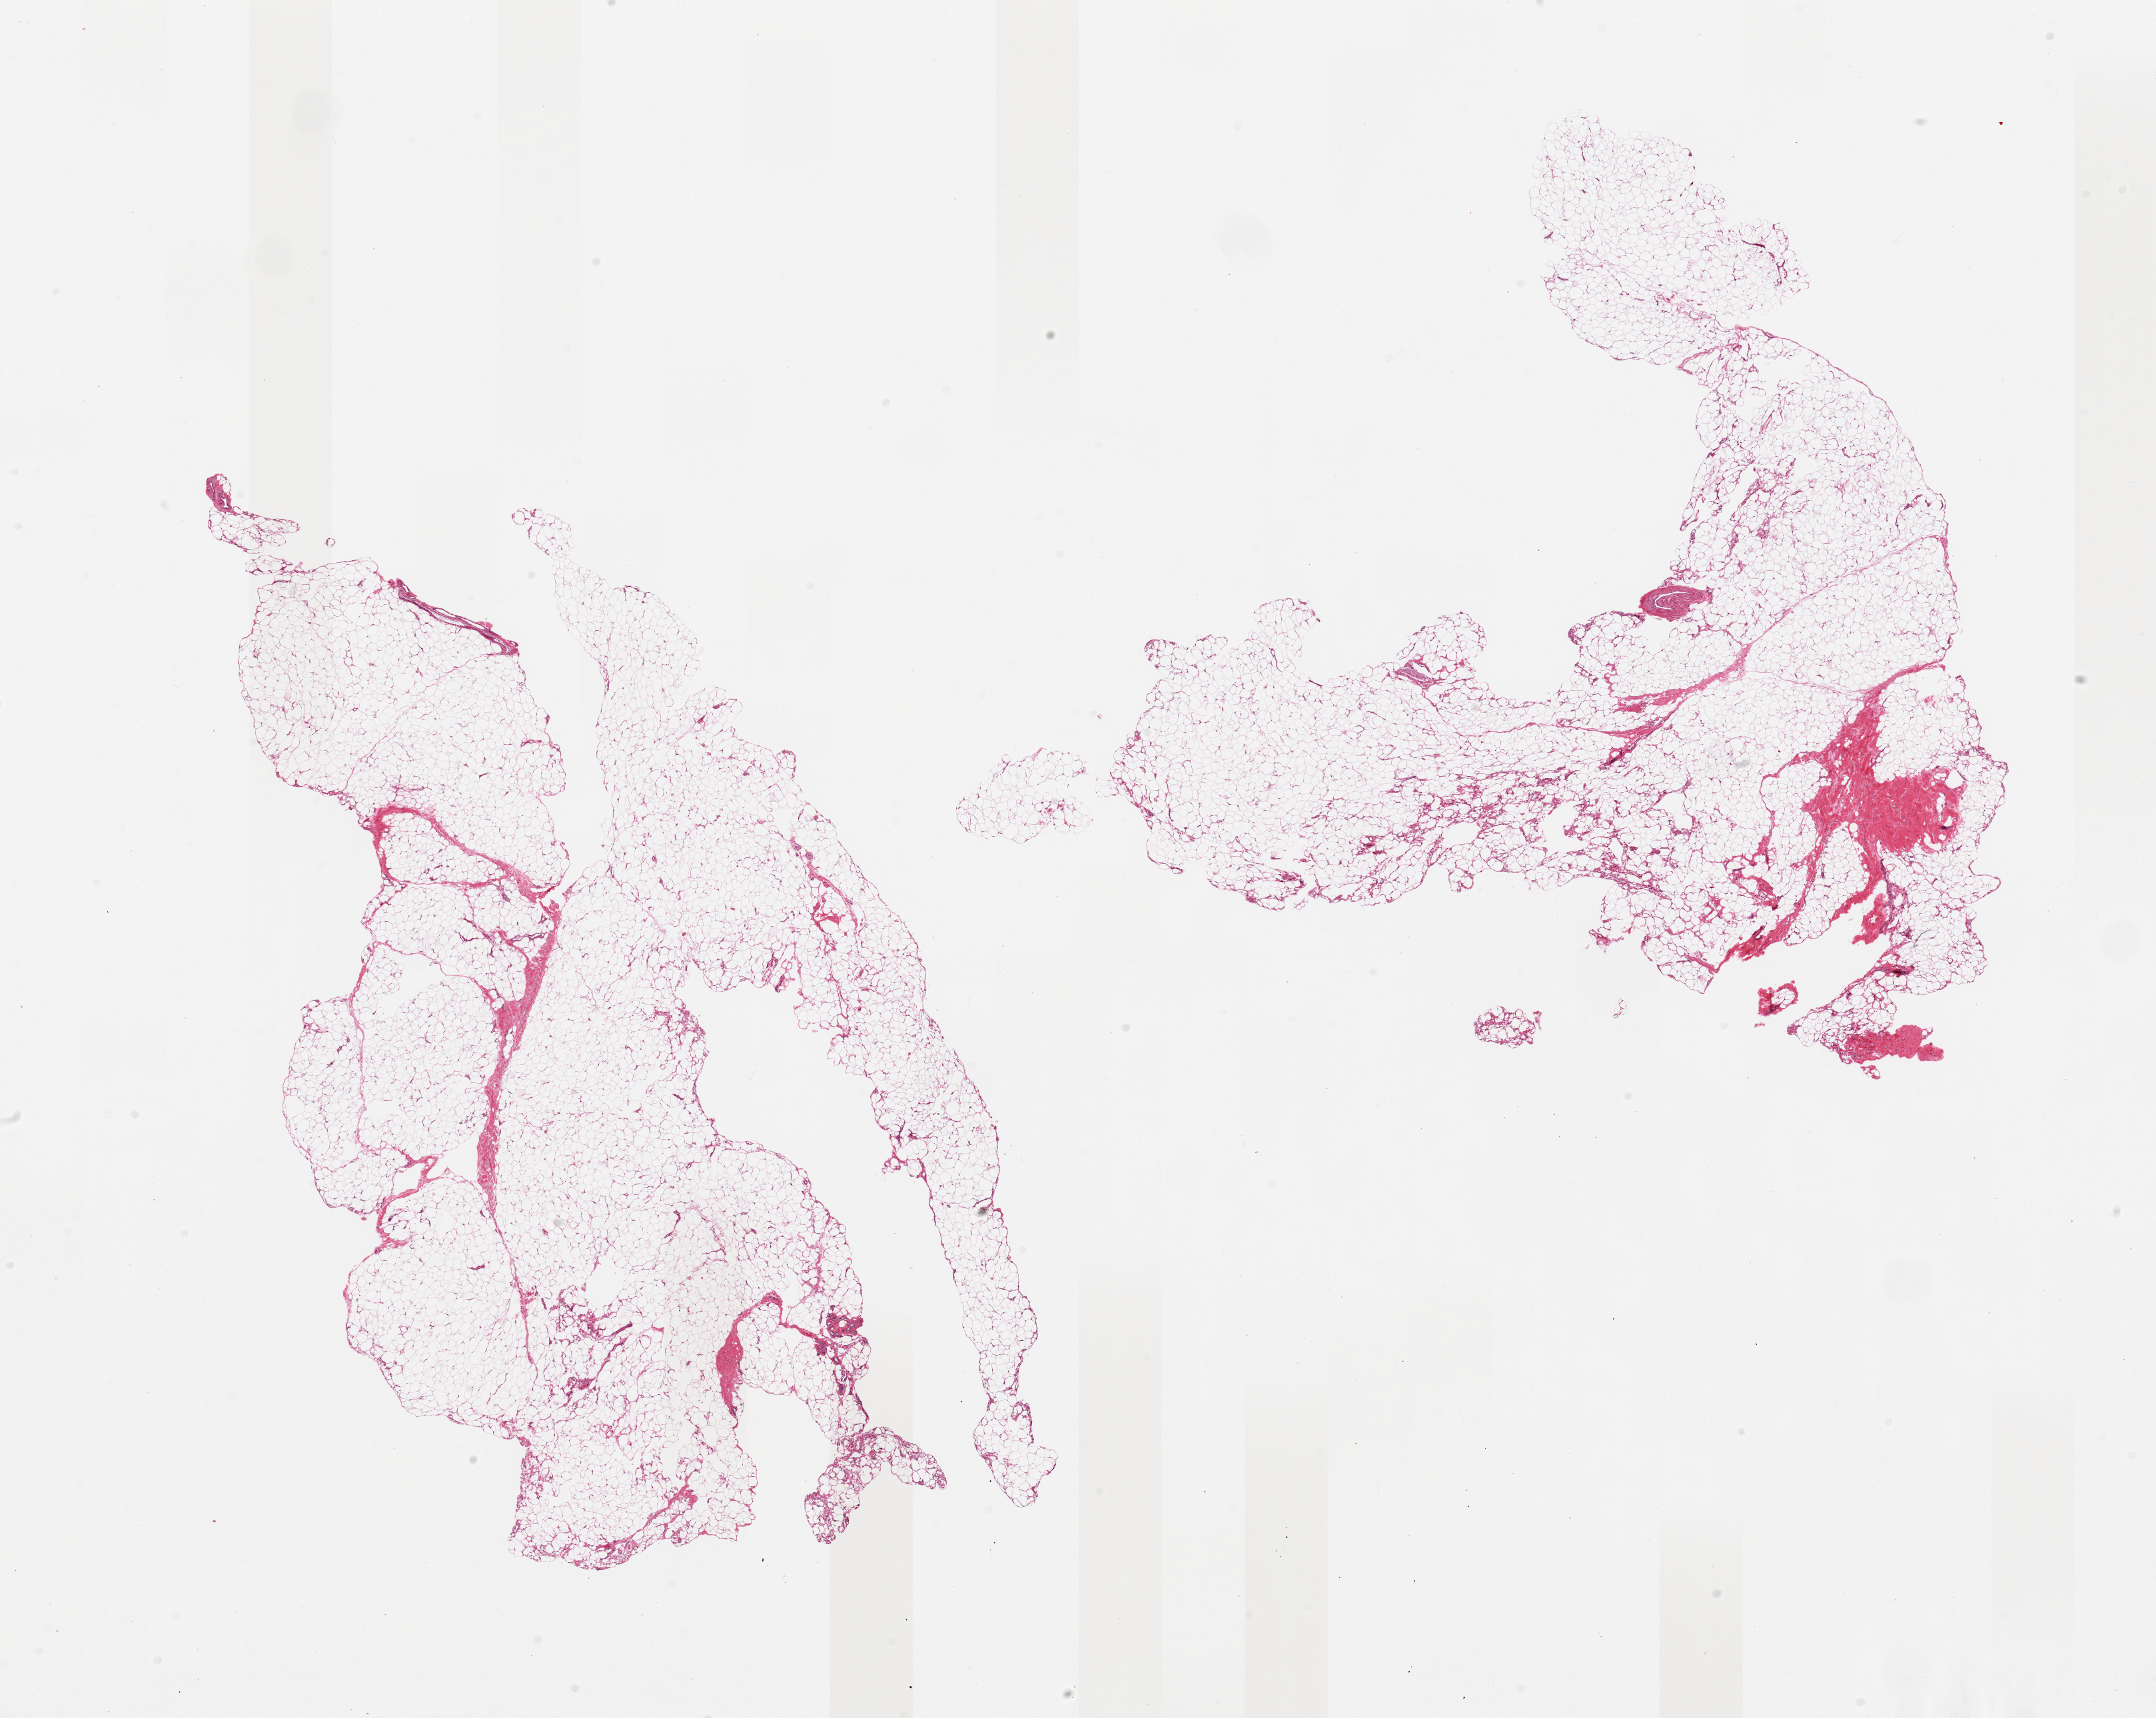
Whole-slide image, hematoxylin and eosin (H&E) stain — a low-resolution overview of the entire scanned area, about 25.6 x 20.4 mm; PAXgene-fixed paraffin-embedded (PFPE) section; target tissue: adipose tissue; tissue donor sample. Female donor.
* pathologist's review note for this sample: 2 pieces; 10% fibrous content